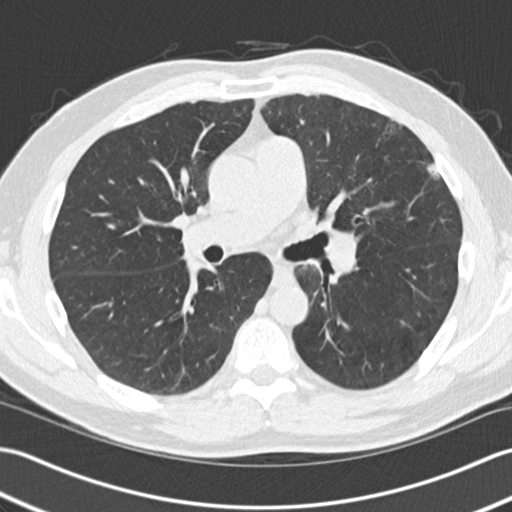
Low-dose screening chest CT, one axial slice. Slice 74 of 140 in the series (ordered by position). Reconstruction kernel B30f. 120 kVp. Lung window (W 1500 / L -600 HU). 512 × 512 image matrix, field of view 352 × 352 mm.
Outlined on this slice (outlined manually by an expert reader):
- lesion 1 (tumor, upper lobe of left lung): bounding box [x1, y1, x2, y2] px = [427, 163, 441, 179]